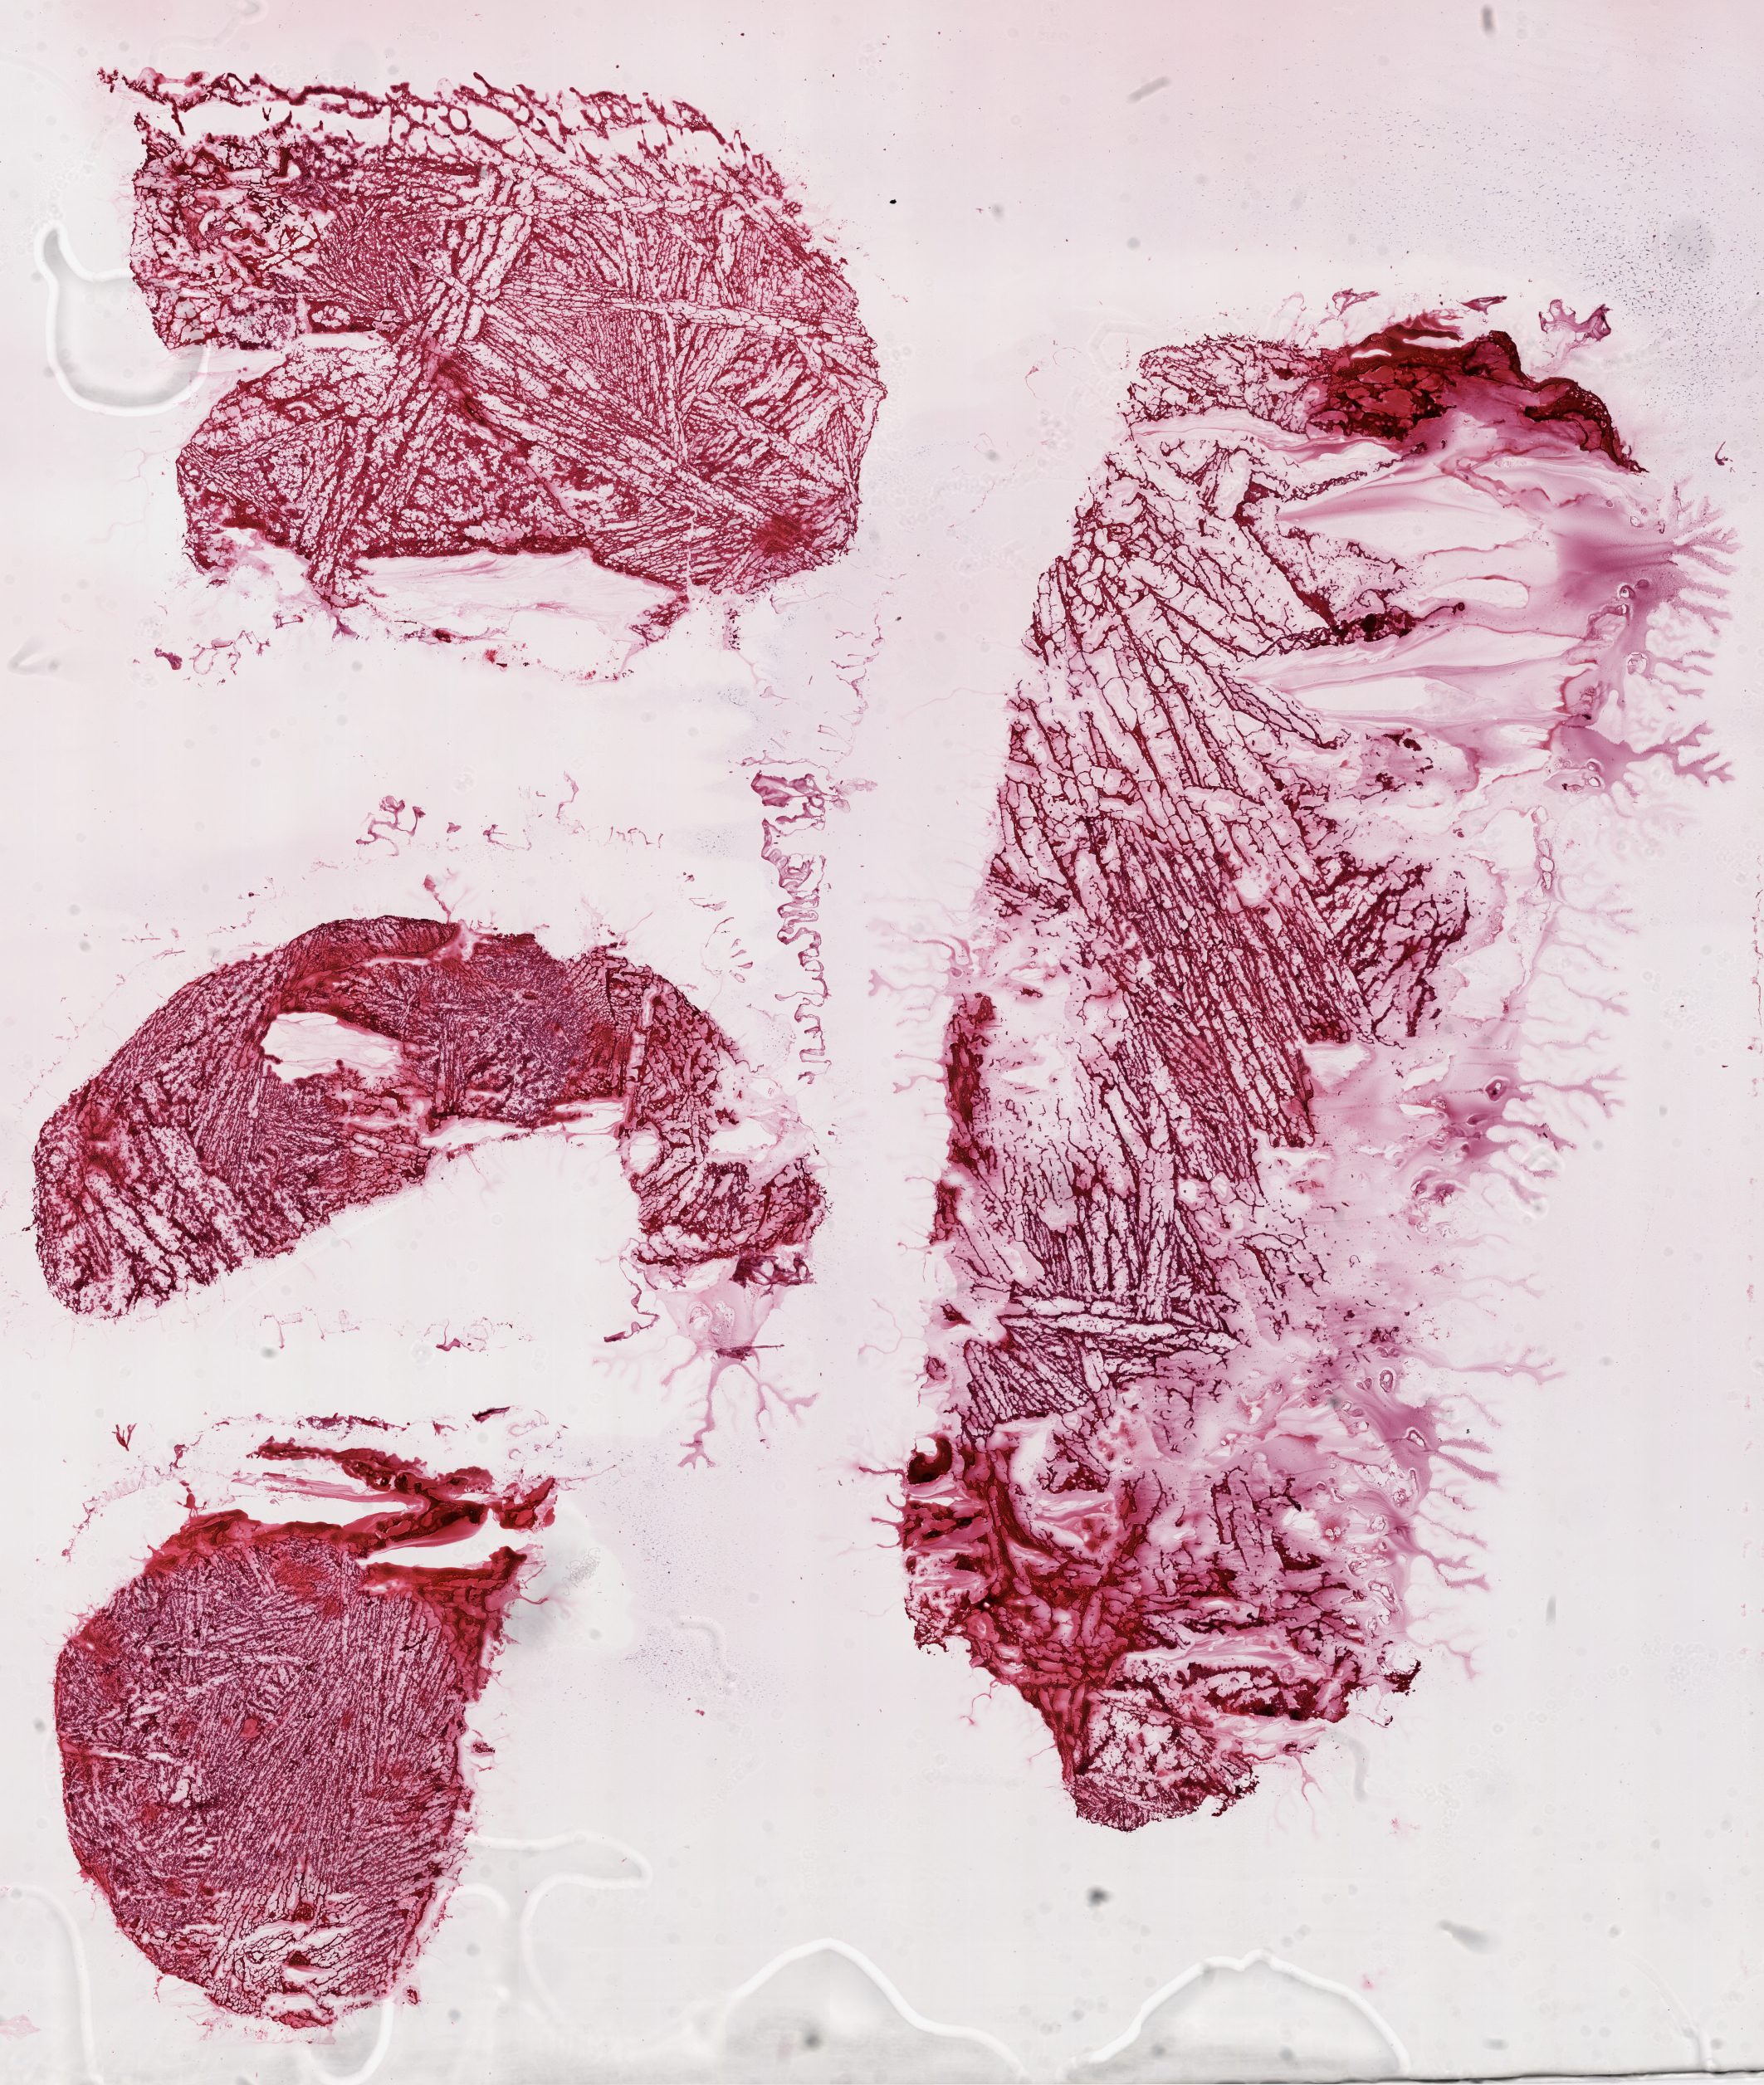
Hematoxylin and eosin (H&E) stained whole-slide image, shown as a low-resolution overview of the whole scanned area (about 17.1 x 20.2 mm). Frozen section from the top of the tissue portion. Brain, primary tumour sample. Male patient; age at initial diagnosis 58 years. Slide review estimates, as recorded: tumour cells 80%, tumour nuclei 70%, normal cells 0%, stromal cells 0%, necrosis 20%.
Pathologic diagnosis: Glioblastoma.